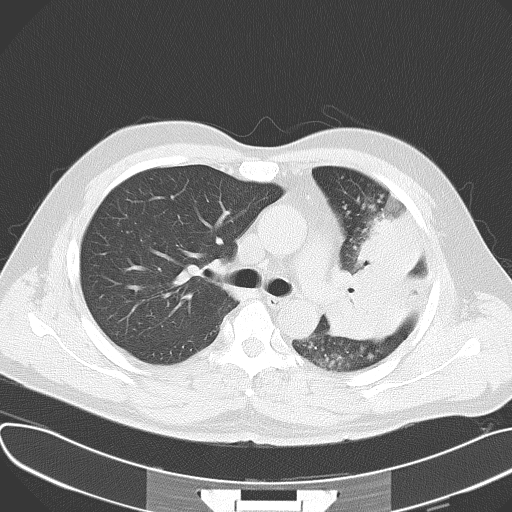
Chest CT, one axial slice; slice 41 of 62 in the series (ordered by position); lung window (W 1500 / L -600 HU); 5 mm slice thickness; 512 × 512 image matrix, field of view 377 × 377 mm. Patient: male, 48 years. From the clinical record (not read from this slice): clinical TNM (as recorded): T4 N0 M0.
Outlined on this slice (bounding box drawn by a radiologist):
- lung tumour (recorded histology: adenocarcinoma): bounding box (x1, y1, x2, y2) in pixels: (330, 199, 426, 351)